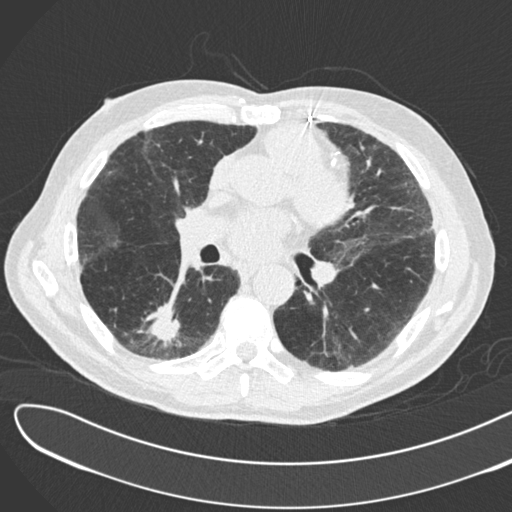
Low-dose screening chest CT, one axial slice. Position 89 of 183 along the scan axis. 120 kVp. Lung window (W 1500 / L -600 HU). 2 mm slice thickness. 512 × 512 image matrix, field of view 370 × 370 mm.
Outlined on this slice (outlined manually by an expert reader):
- lesion 1 (tumor, lower lobe of right lung): bounding box (x1, y1, x2, y2) in pixels: (150, 301, 180, 343)